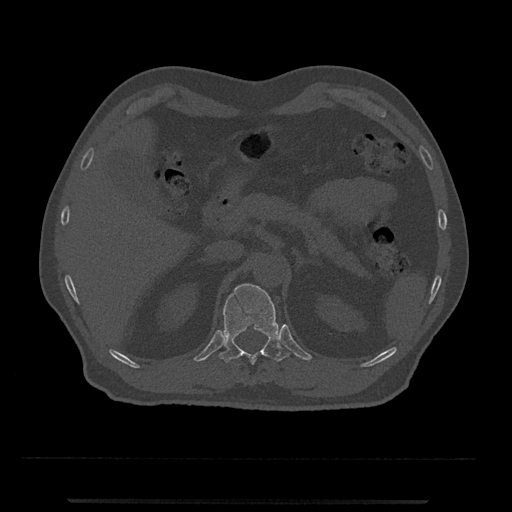
CT including the spine, one axial slice; slice 408 of 797 in the series (ordered by position); bone window (W 1800 / L 400 HU); 512 × 512 image matrix. Patient: male, 63 years. From the clinical record (not read from this slice): primary cancer: prostate.
Outlined on this slice (semi-automatic segmentation, software-assisted and operator-edited):
- T12 vertebra: bounding box (x1, y1, x2, y2) in pixels: (219, 283, 289, 365)